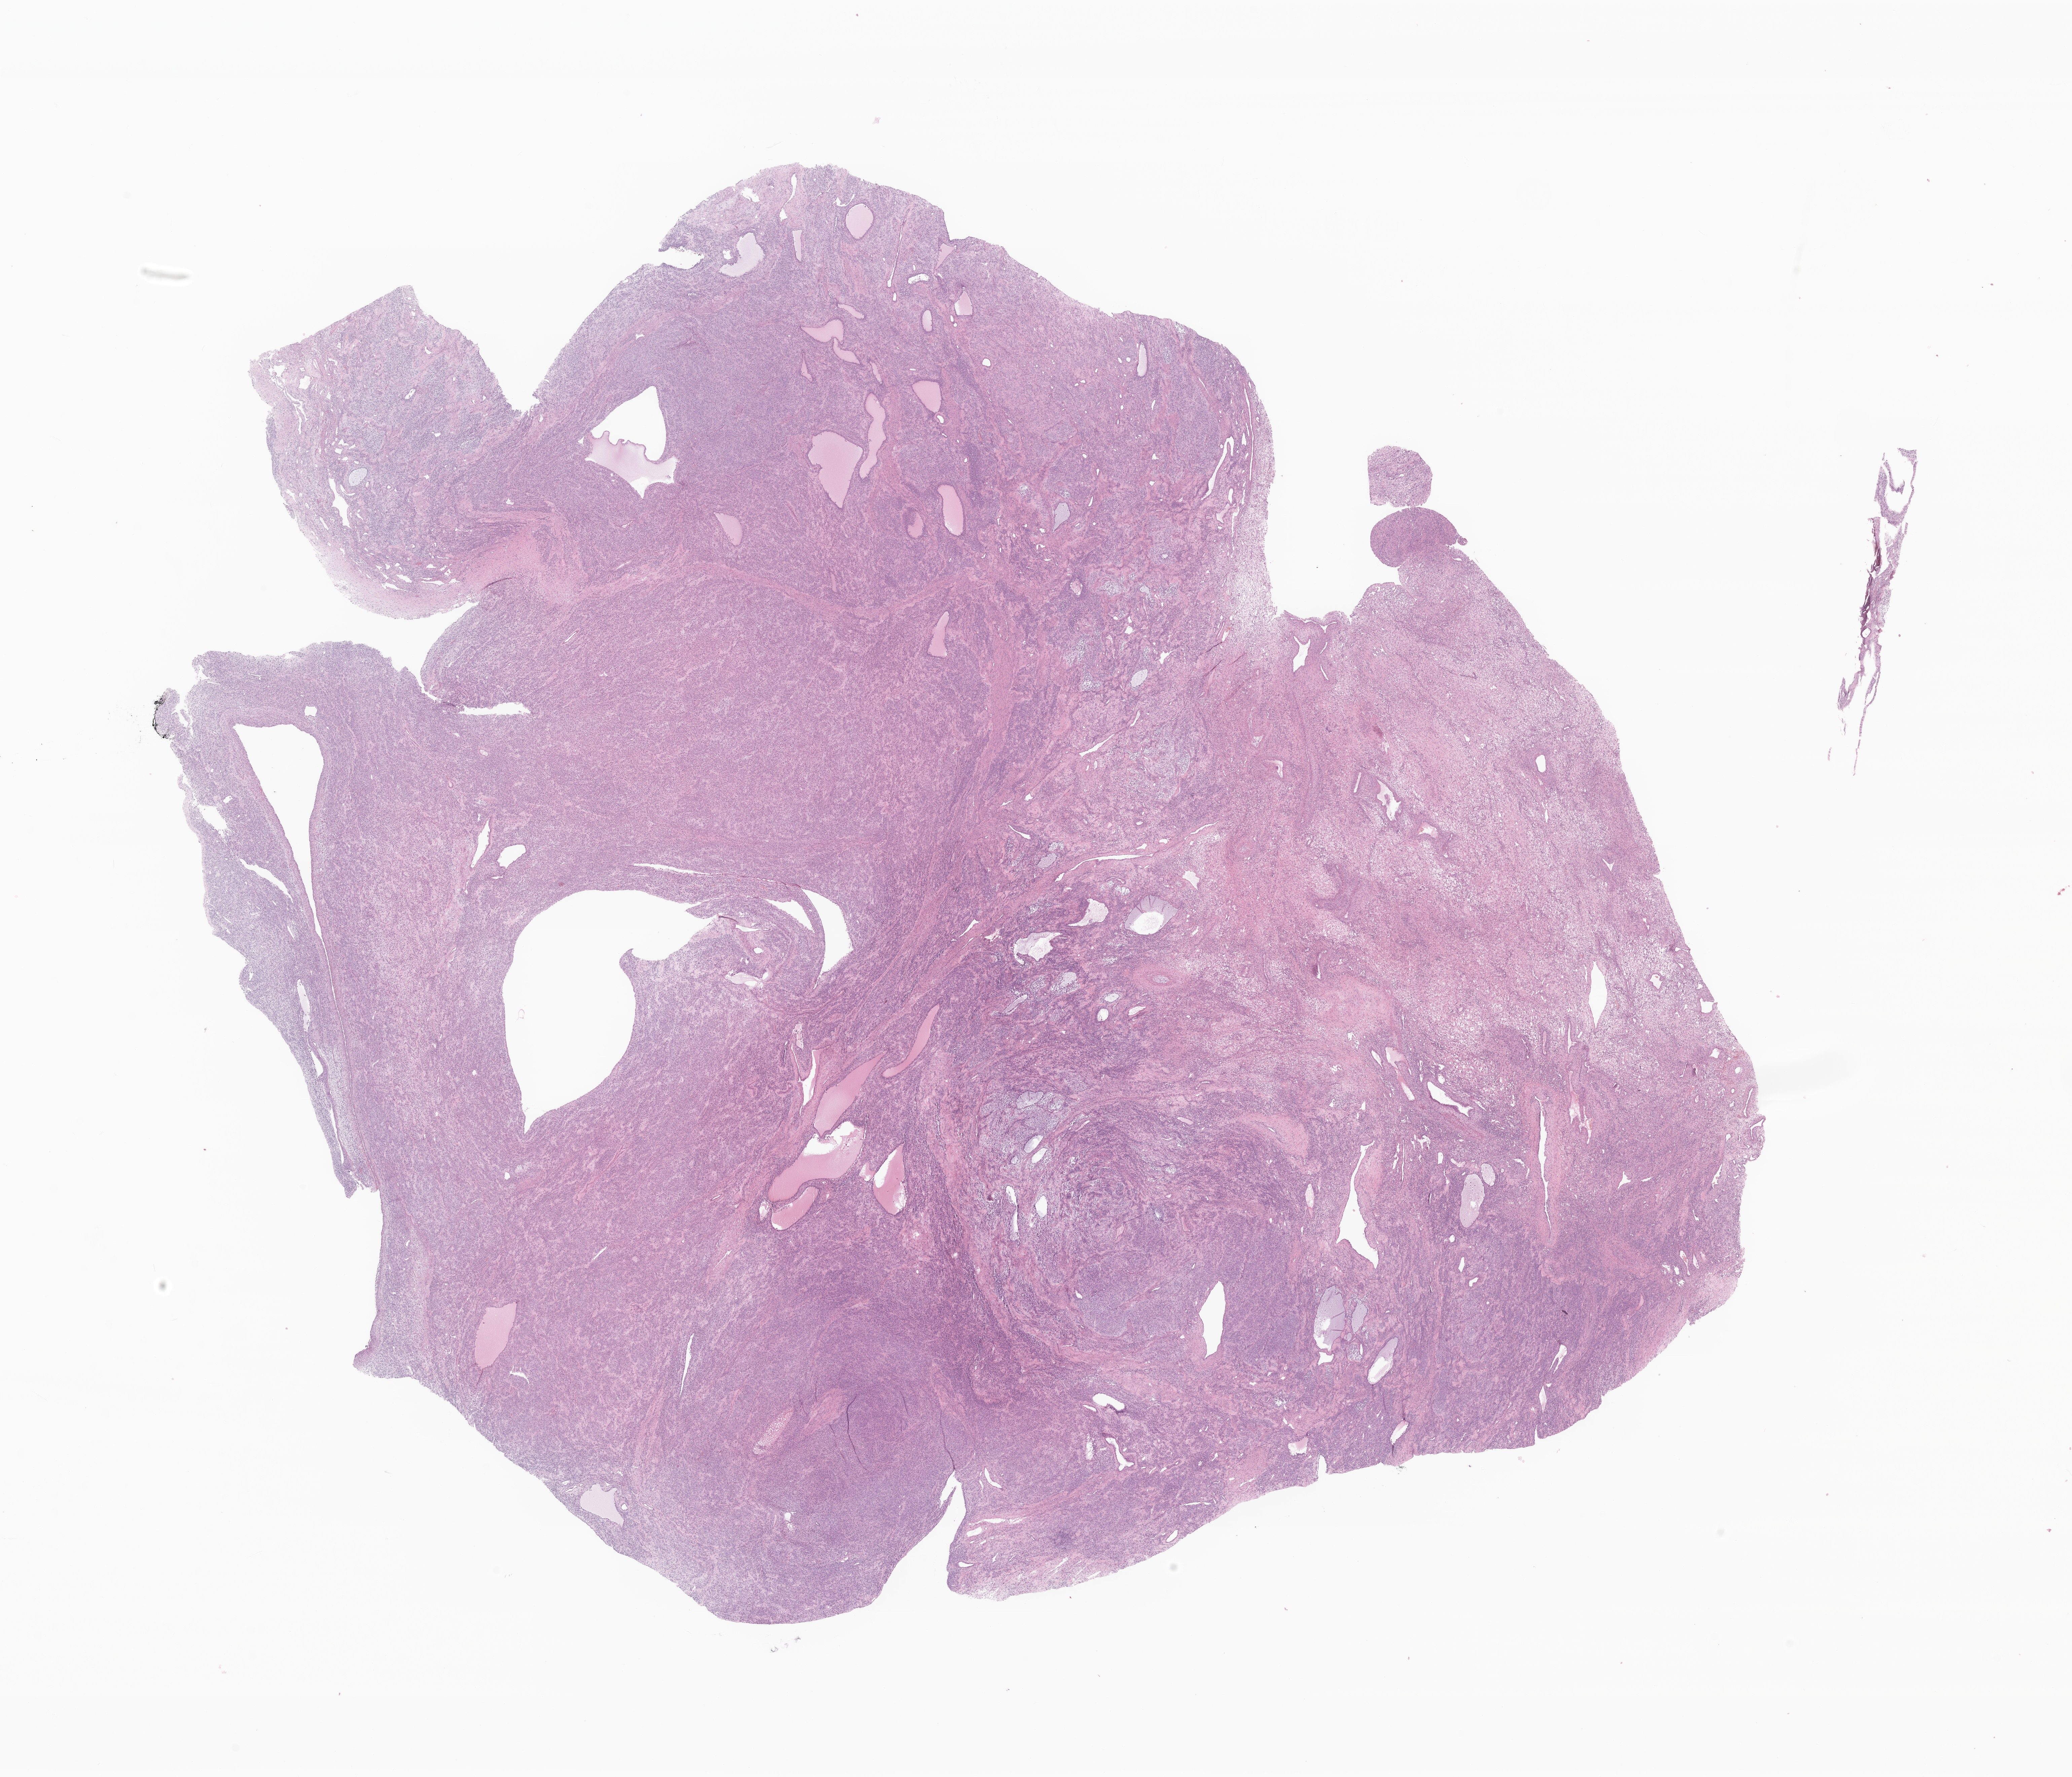
H&E whole-slide image of tumor tissue from the ovary, low-resolution overview of the scanned area, about 26.0 x 22.3 mm; formalin-fixed, paraffin-embedded (FFPE) tissue. Patient: female, age 156 months (13 years).
• recorded diagnosis: Sex cord-gonadal stromal tumor, NOS